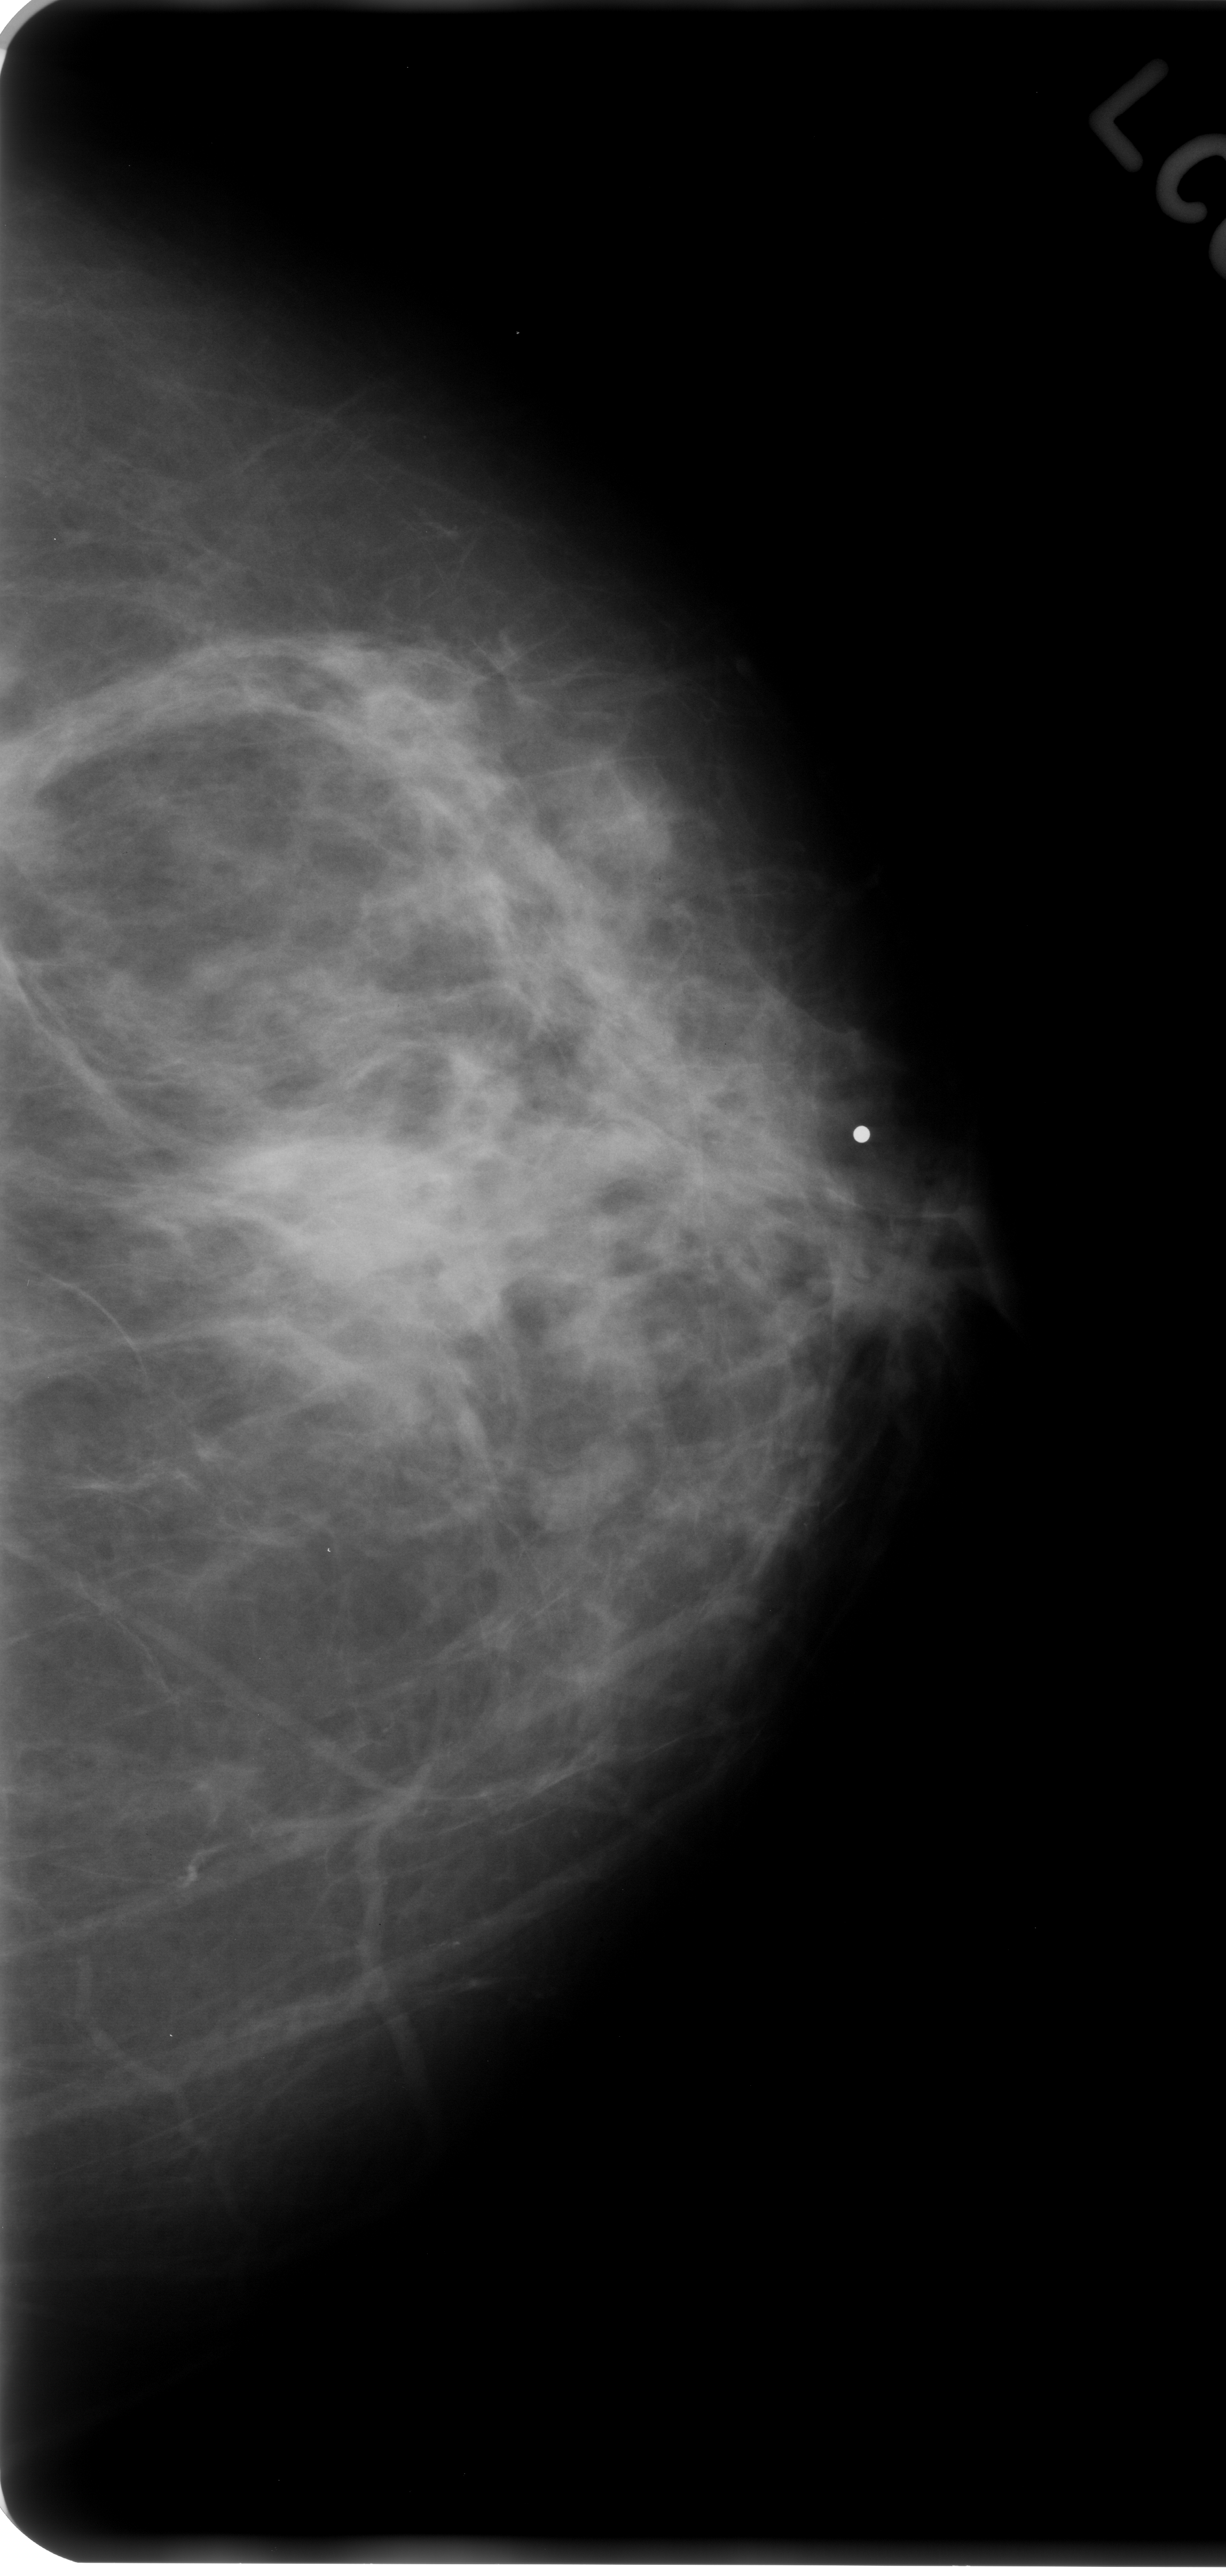
Scanned film-screen mammogram, left breast, craniocaudal (CC) view, BI-RADS breast density category 2 (scale 1–4).
Marked findings (only marked abnormalities are described; nothing is implied about the rest of the image): mass, shape irregular, margins ill defined; BI-RADS assessment category 4; subtlety rating 4 on a 1 (subtle) to 5 (obvious) scale; pathology (as recorded): malignant.